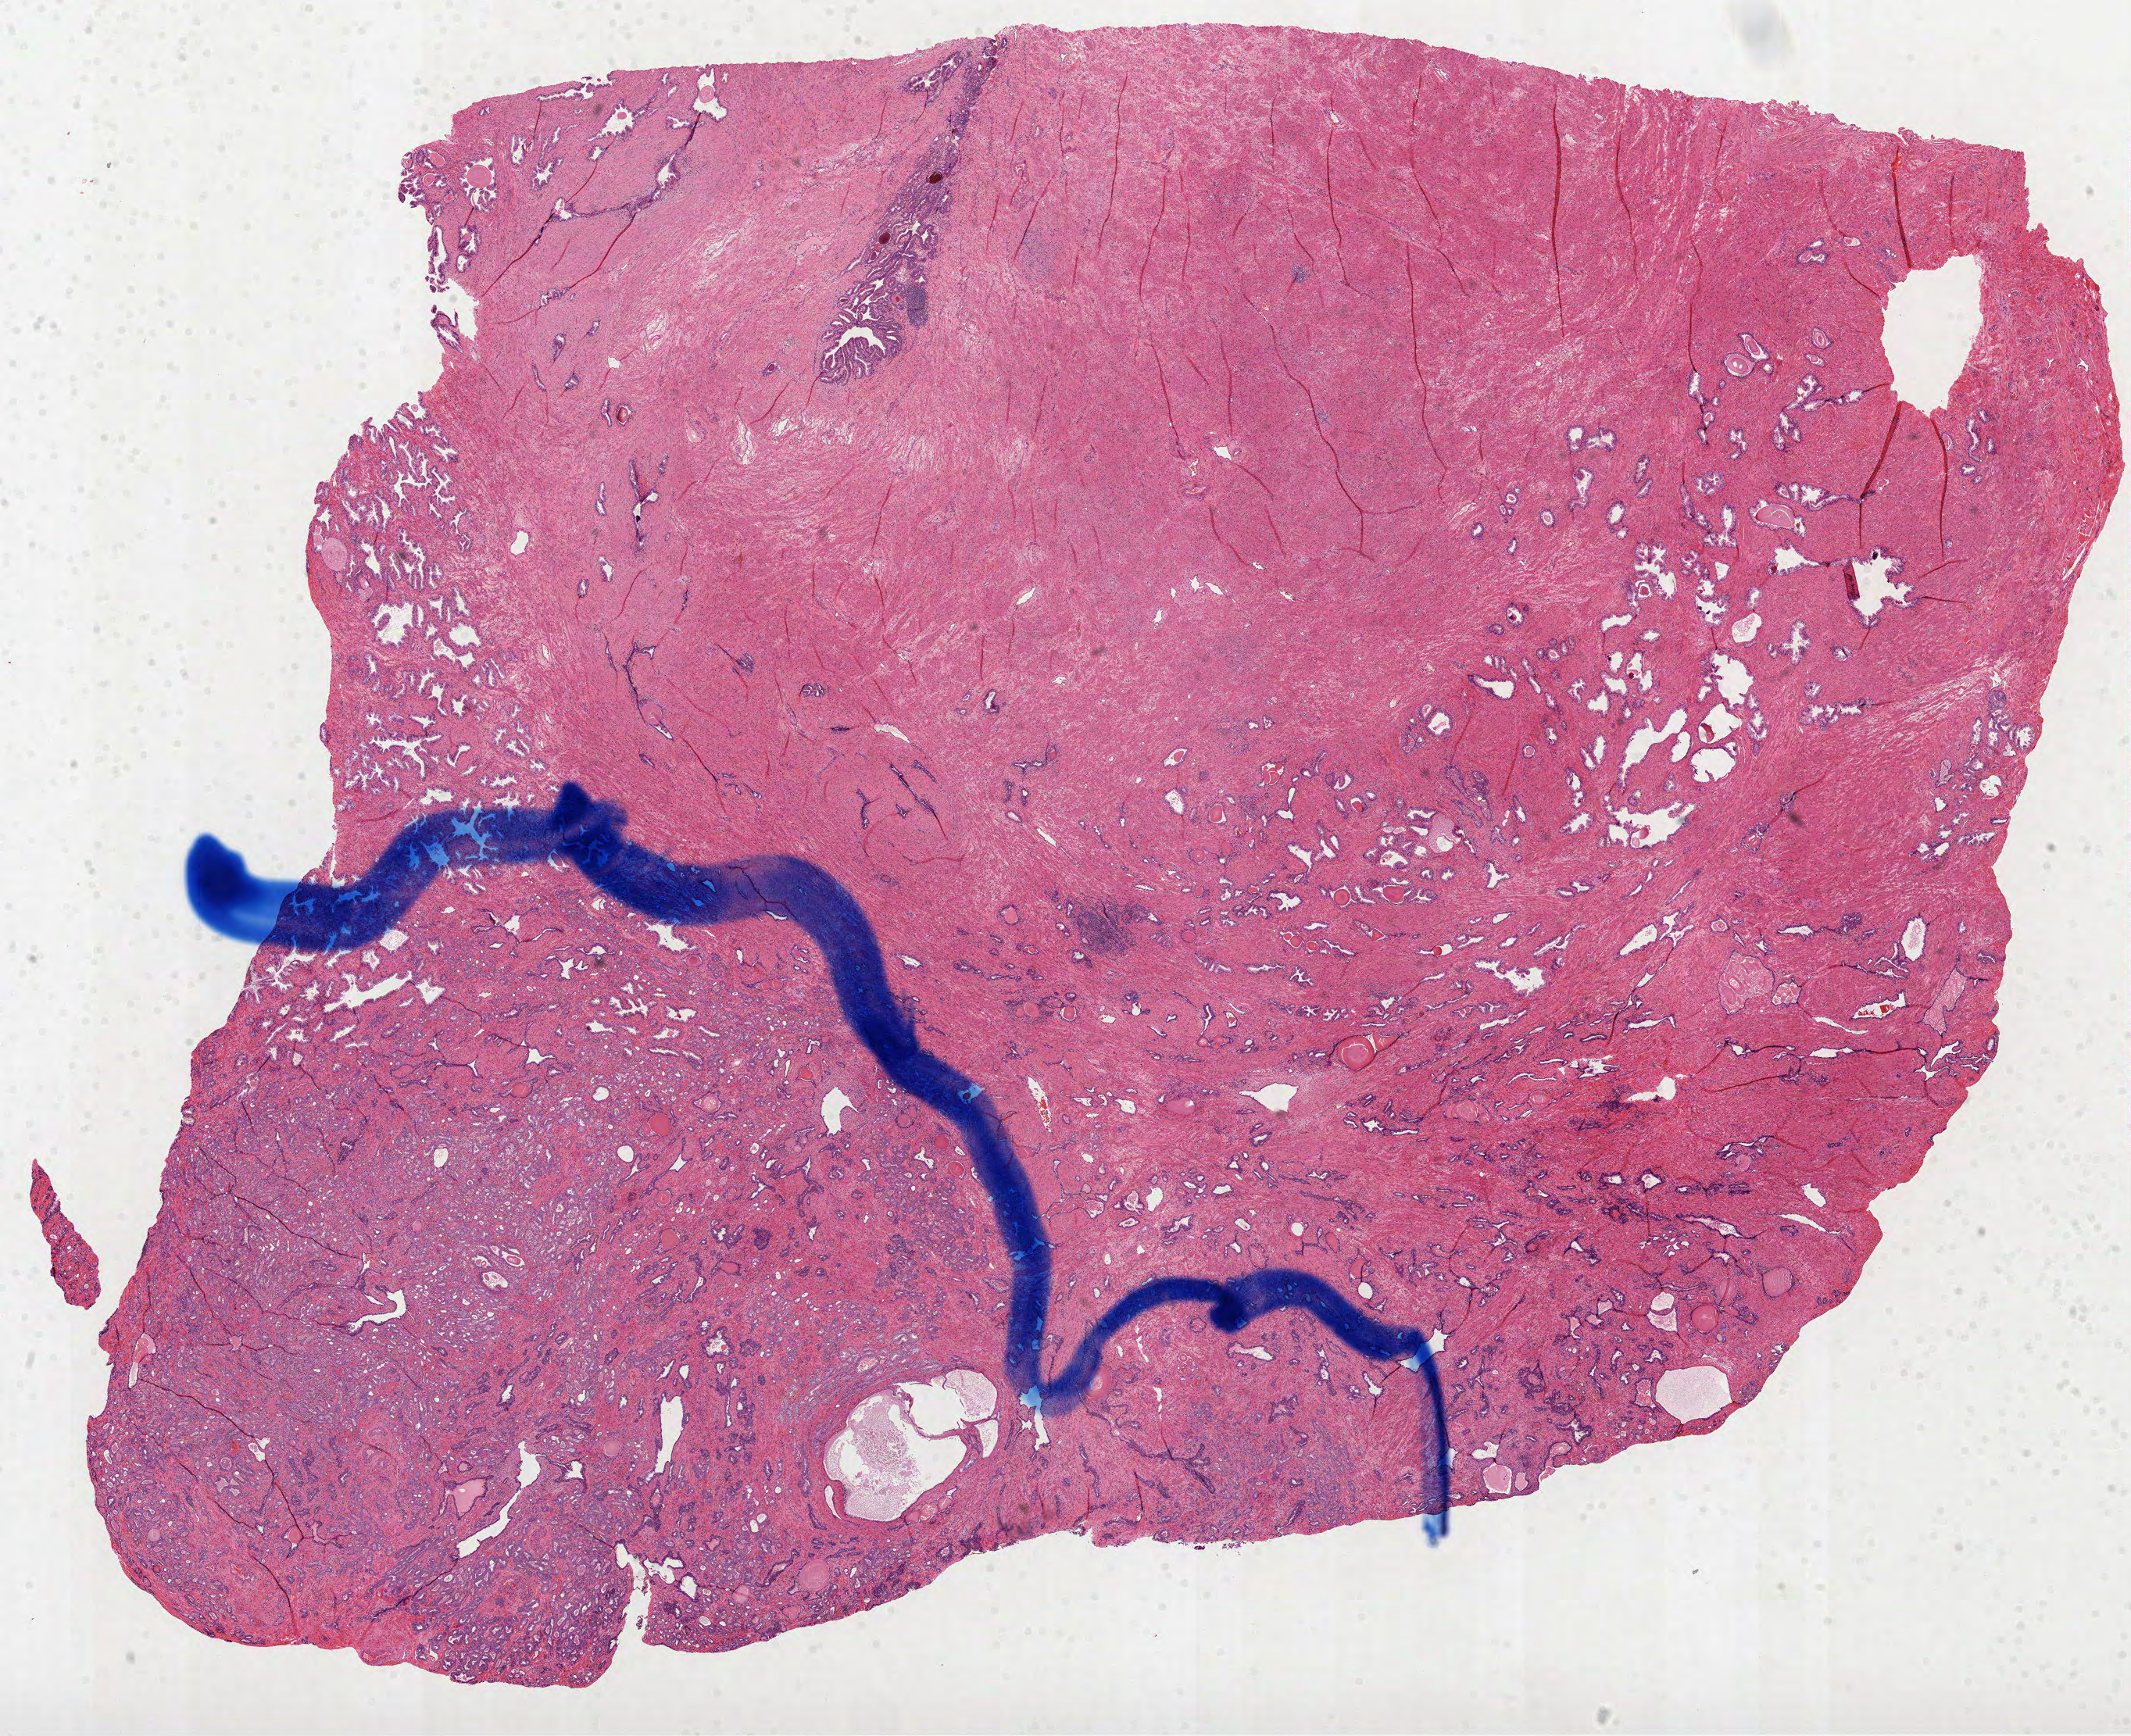
H&E whole-slide image, low-resolution overview of the scanned area, about 22.0 x 17.9 mm (acquisition: 40x scan), FFPE section, sample: primary tumour, prostate. Male patient; age at initial diagnosis 63 years. Gleason score: 7 (3+4).
Lymph nodes positive (case pathology): 0 of 10 examined. Diagnosis: Acinar cell carcinoma (prostate gland).